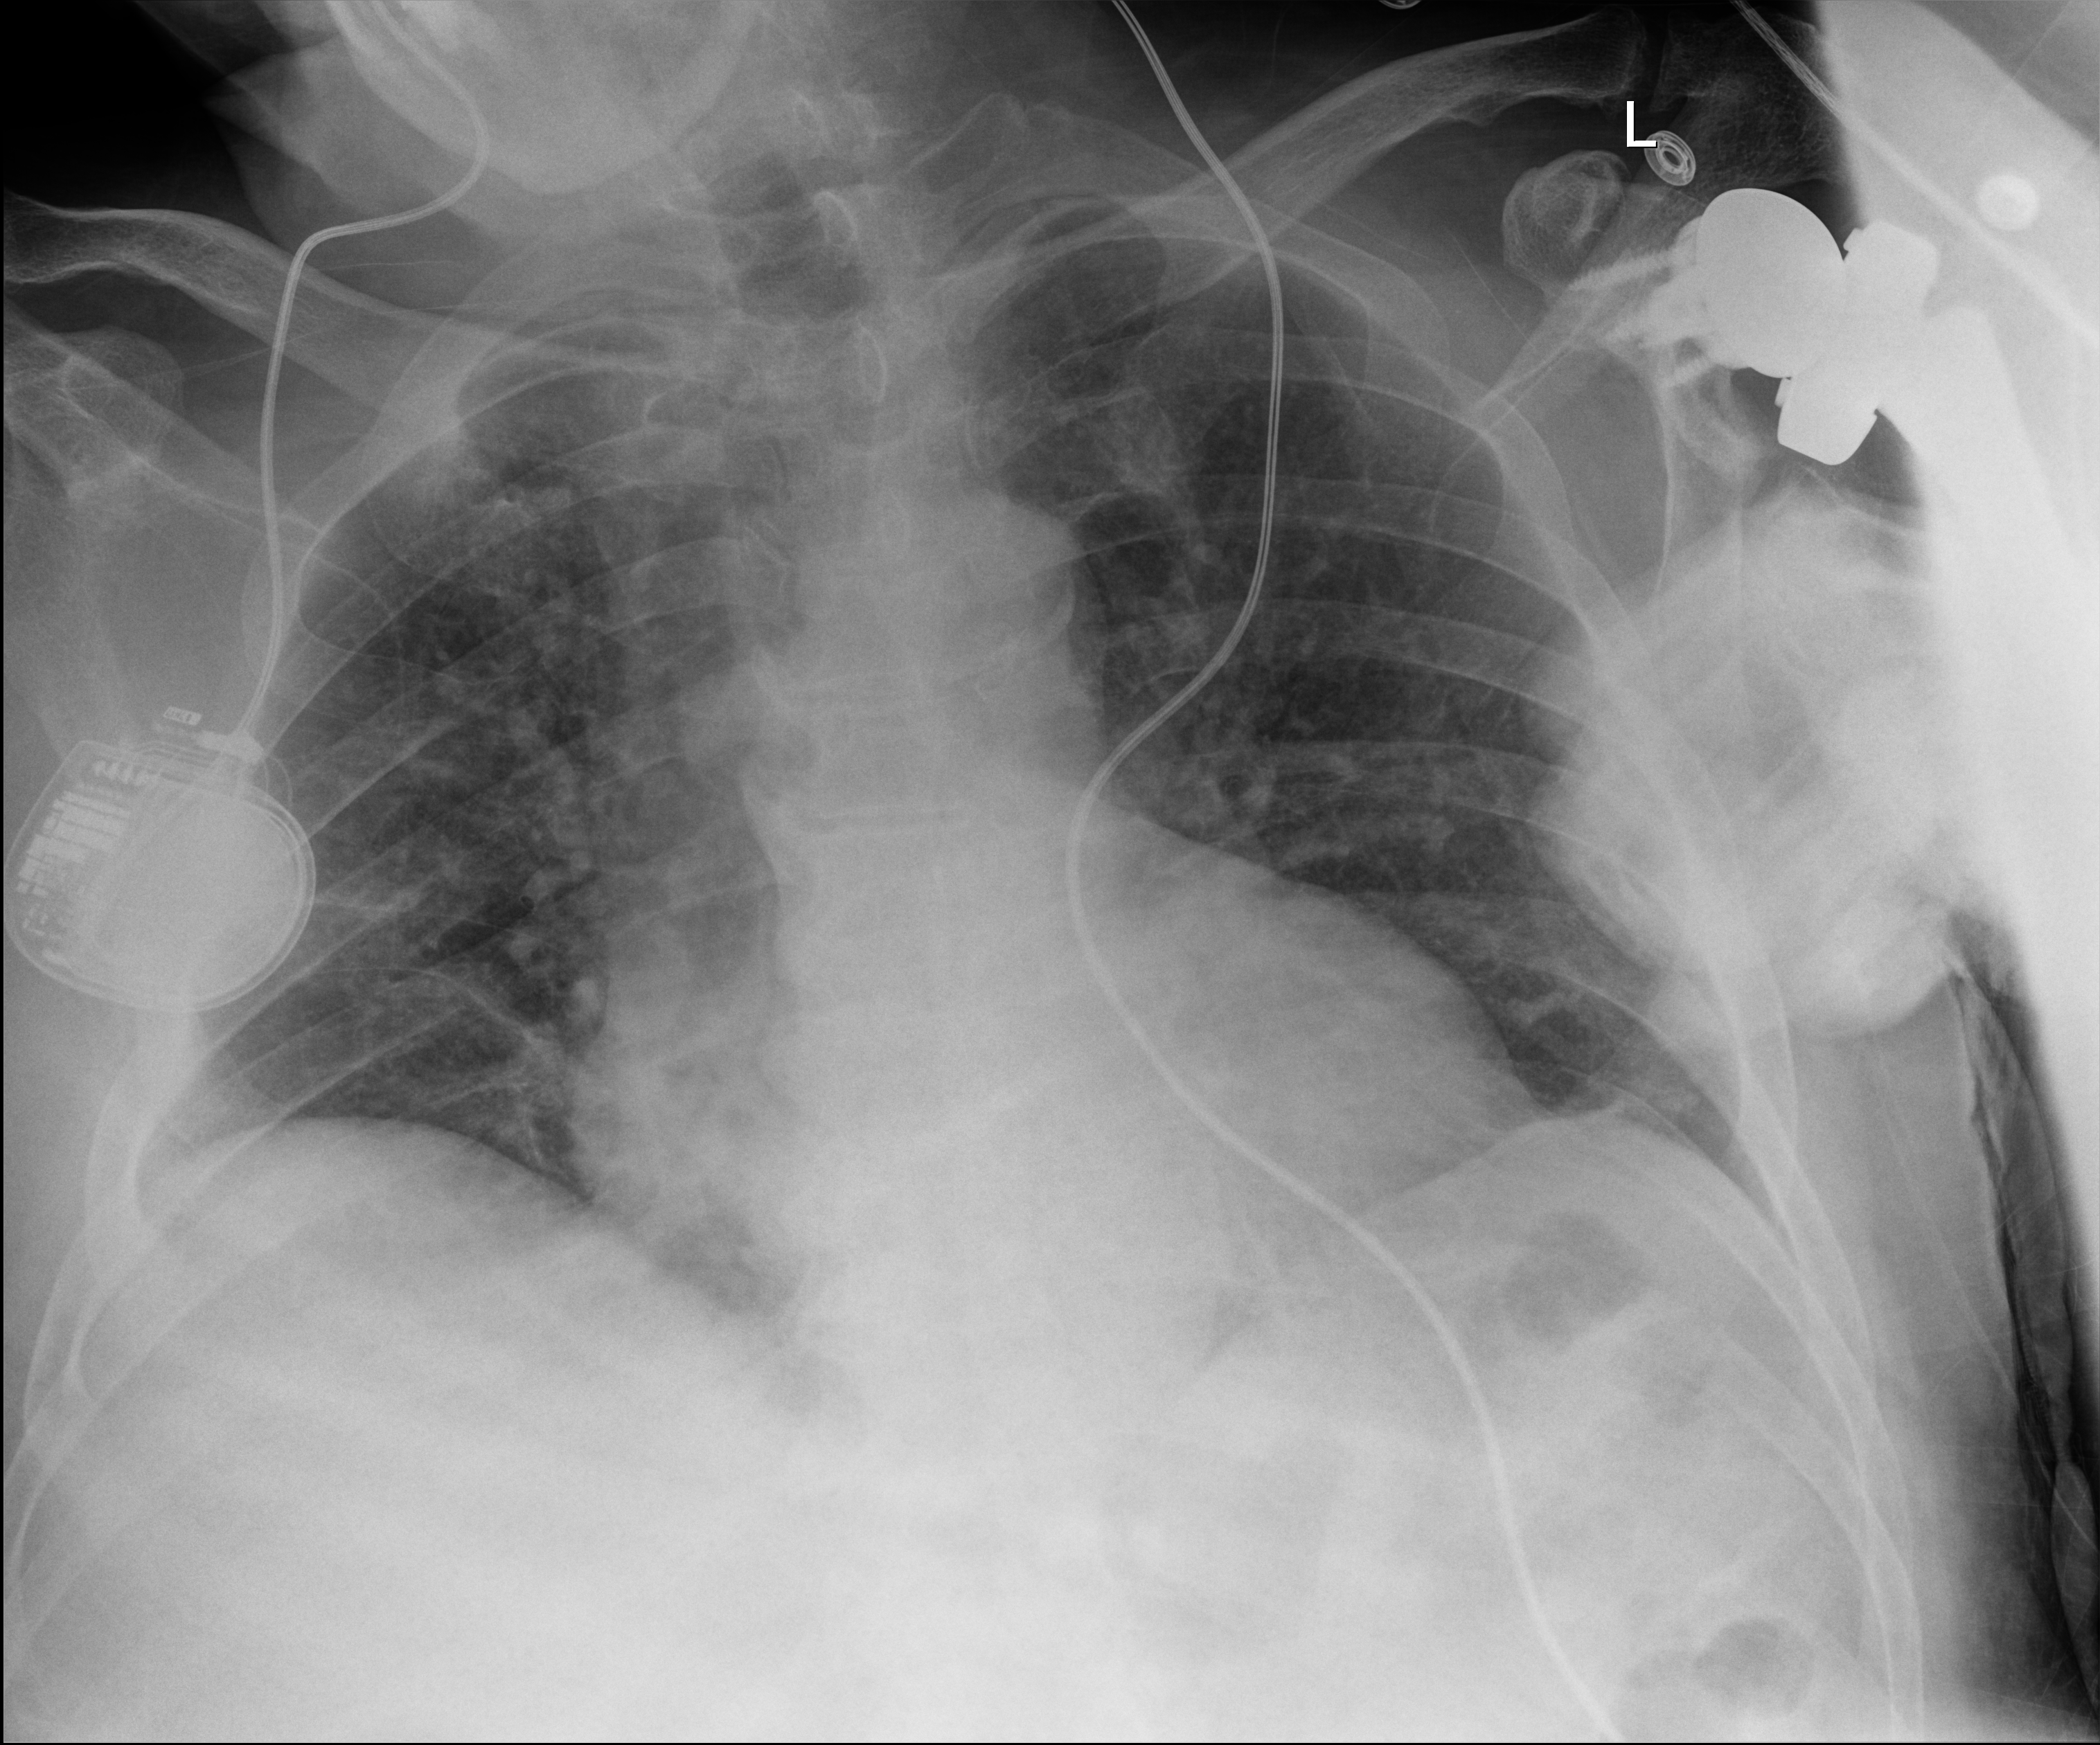
Bedside chest radiograph (digital radiography); anteroposterior (AP) projection. Patient hospitalised with COVID-19; male, aged 60–74 years.
Hospital-stay facts (about this admission, not read from this image; timing relative to this image not recorded):
- mechanically ventilated during this hospital stay: no